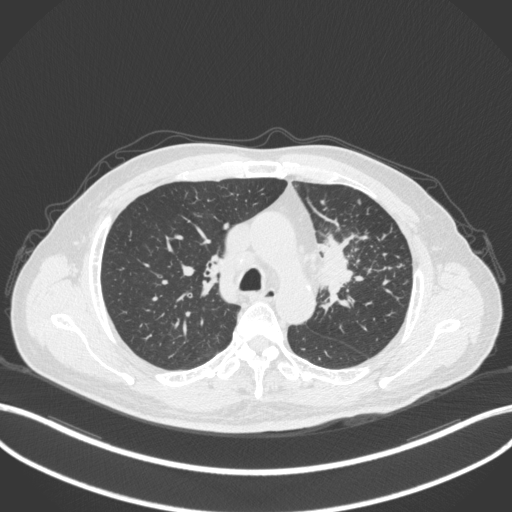
Chest CT, one axial slice; position 241 of 386 along the scan axis; reconstruction kernel B31f; 120 kVp; lung window (W 1500 / L -600 HU); 512 × 512 image matrix, field of view 400 × 400 mm. Male patient, age 69 years. Case-level facts recorded for this patient, not image findings: clinical TNM (as recorded): T2a N2 M0.
Outlined on this slice (bounding box drawn by a radiologist):
- lung tumour (recorded histology: adenocarcinoma): bounding box (x1, y1, x2, y2) in pixels: (319, 236, 362, 318)